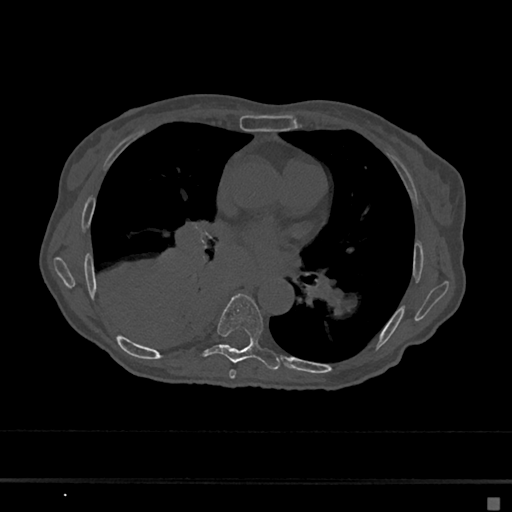
CT including the spine, one axial slice. Slice 374 of 797 in the series (ordered by position). Reconstruction kernel Br40s/3. Bone window (W 1800 / L 400 HU). 0.5 mm slice thickness. 512 × 512 image matrix, field of view 360 × 360 mm. Female patient, age 68 years. Case-level facts recorded for this patient, not image findings: primary cancer: renal.
Outlined on this slice (semi-automatic segmentation, software-assisted and operator-edited):
- T6 vertebra: box from (x=229, y=370) to (x=236, y=379) px
- T7 vertebra: (x=200, y=294)–(x=280, y=370)